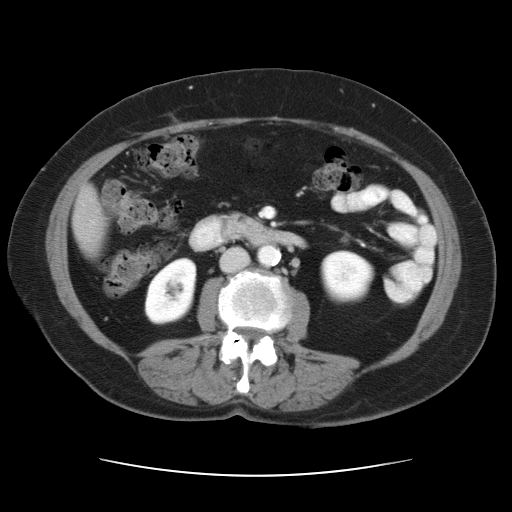
Contrast-enhanced abdominal CT, one axial slice; position 8 of 34 along the scan axis; 120 kVp; intravenous contrast given; soft-tissue window (W 400 / L 40 HU); 512 × 512 image matrix, field of view 360 × 360 mm. Female patient, age 65 years. From the clinical record (not read from this slice): diagnosis: colorectal cancer liver metastases, imaged before liver resection; multiple liver metastases: yes; largest metastasis: 2.2 cm; disease in both lobes: no.
Outlined on this slice (manually delineated by an expert):
- liver: box from (x=82, y=203) to (x=98, y=240) px
- planned liver remnant (the part of the liver to remain after resection): (x=82, y=203)–(x=98, y=240)